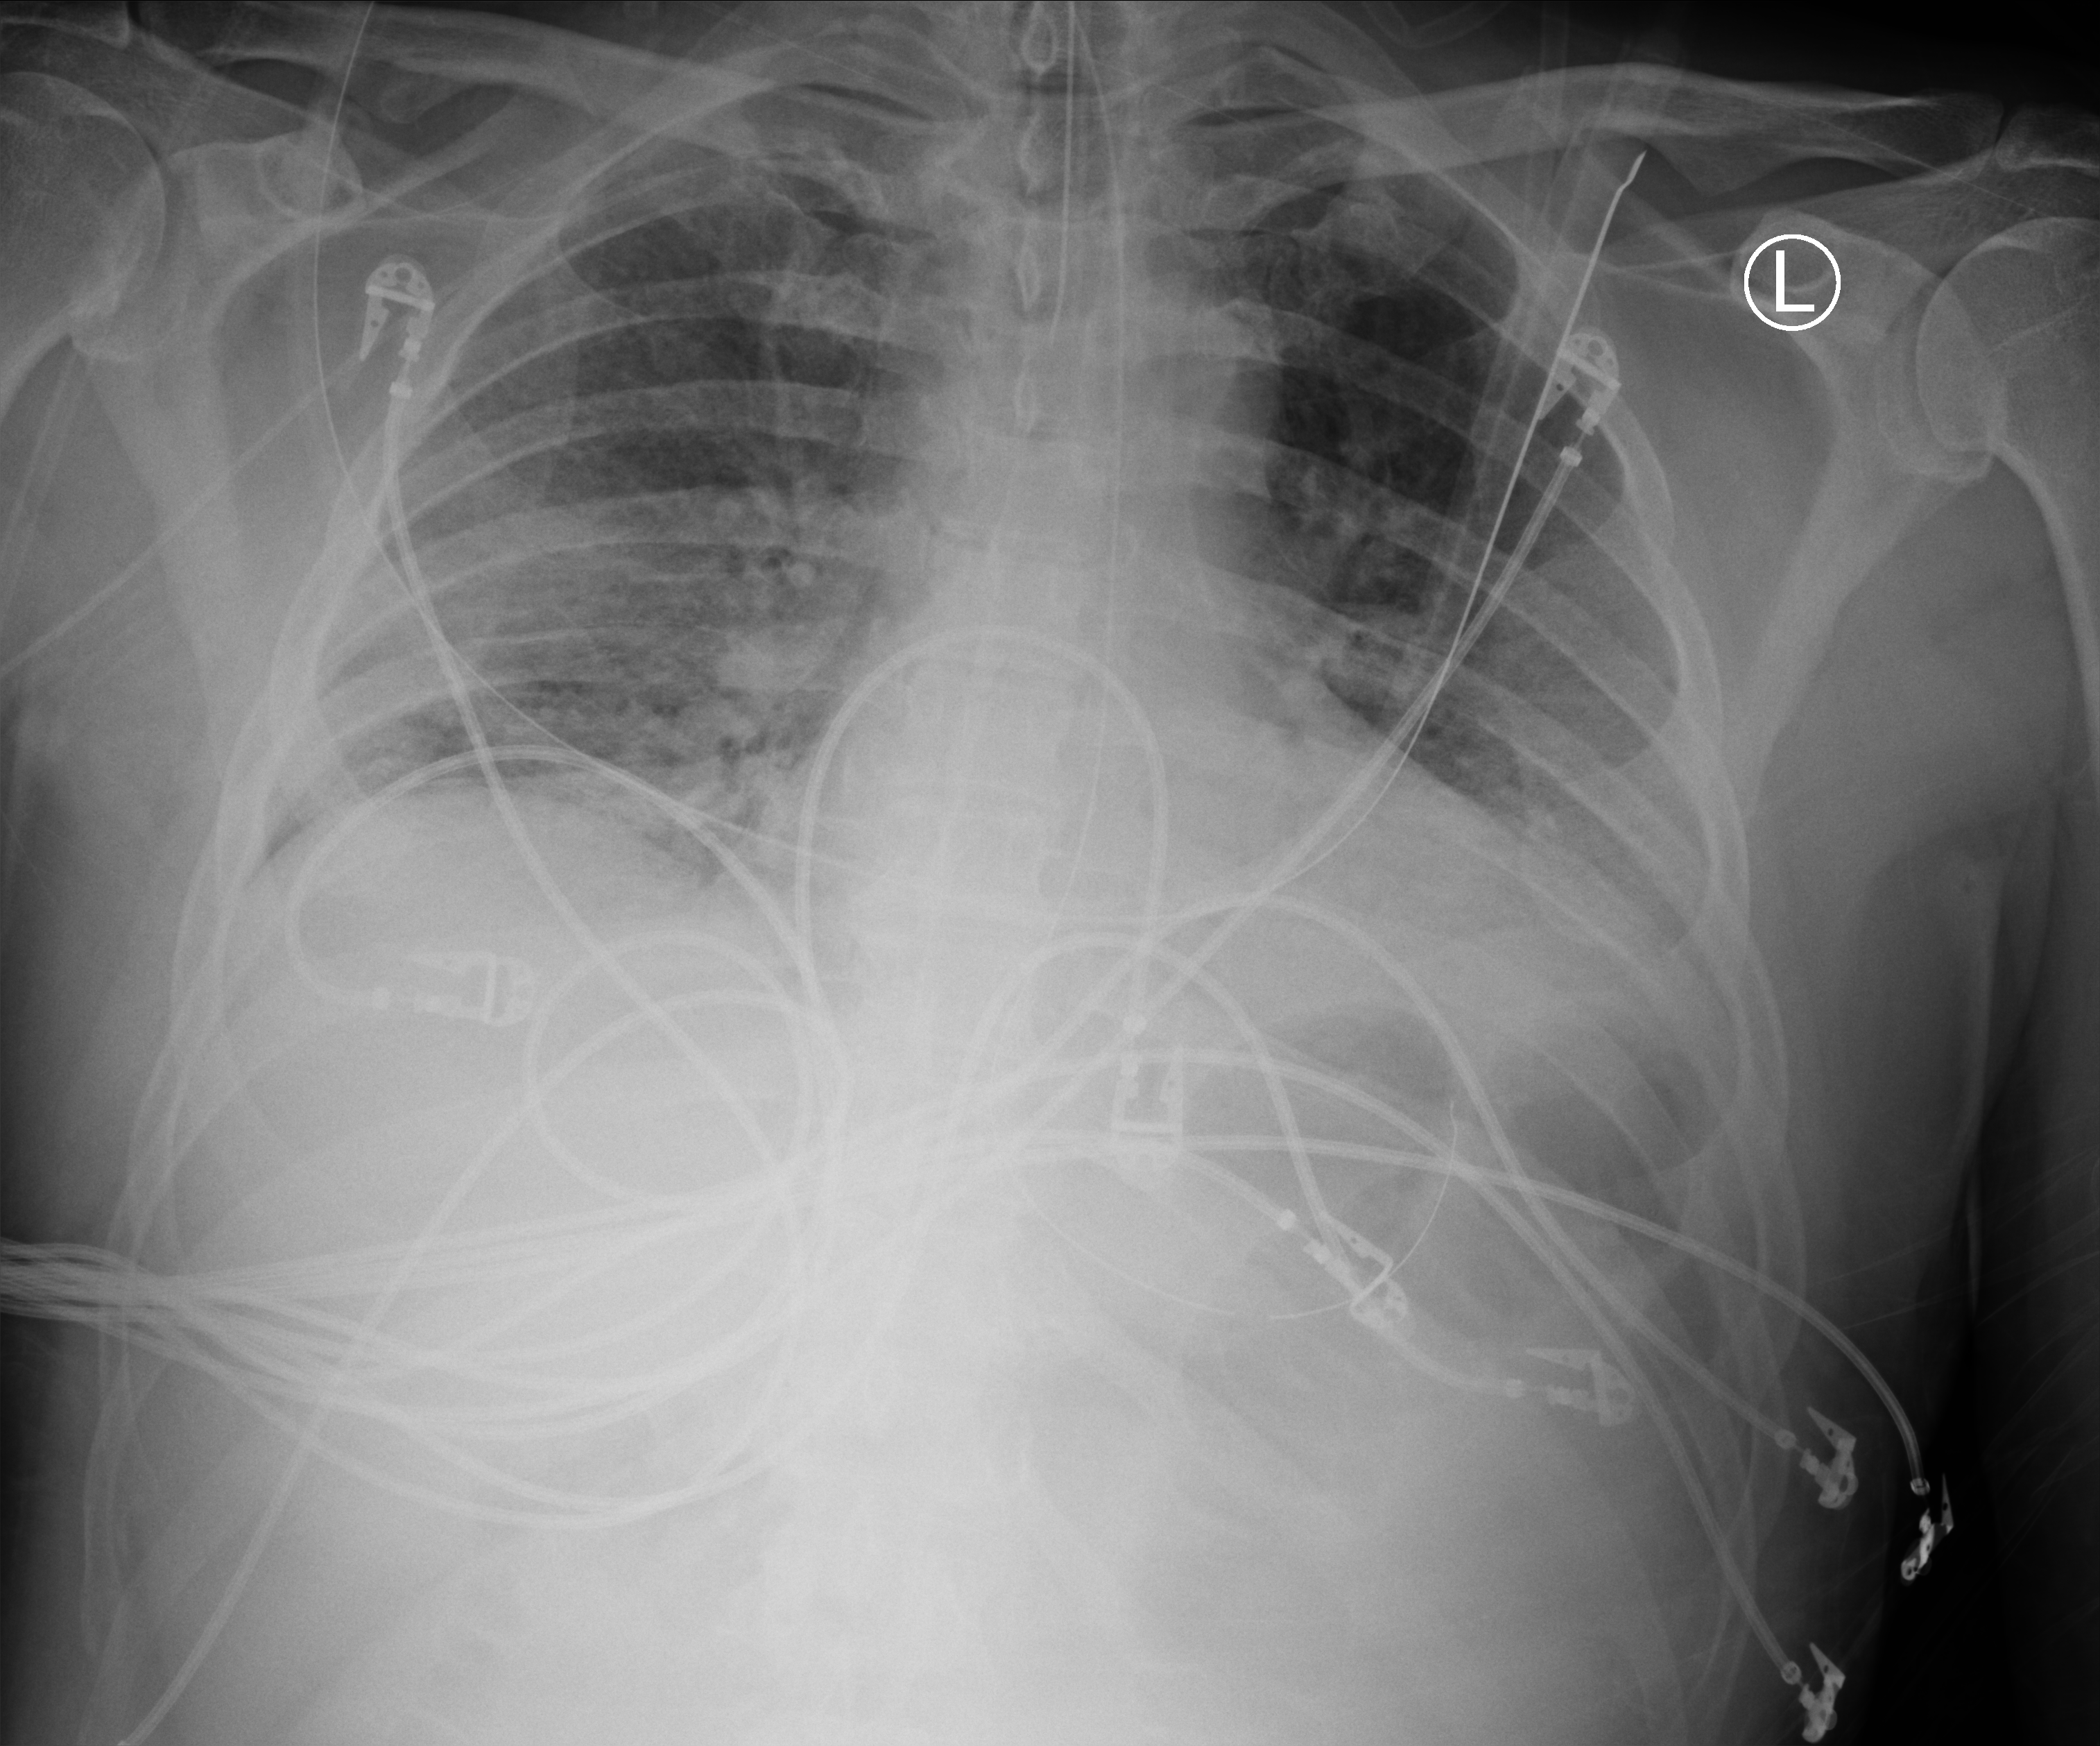
Portable chest radiograph. Patient hospitalised with COVID-19; male, aged 60–74 years.
Hospital-stay facts (about this admission, not read from this image; timing relative to this image not recorded):
- mechanically ventilated during this hospital stay: yes
- admitted to intensive care during this hospital stay: yes